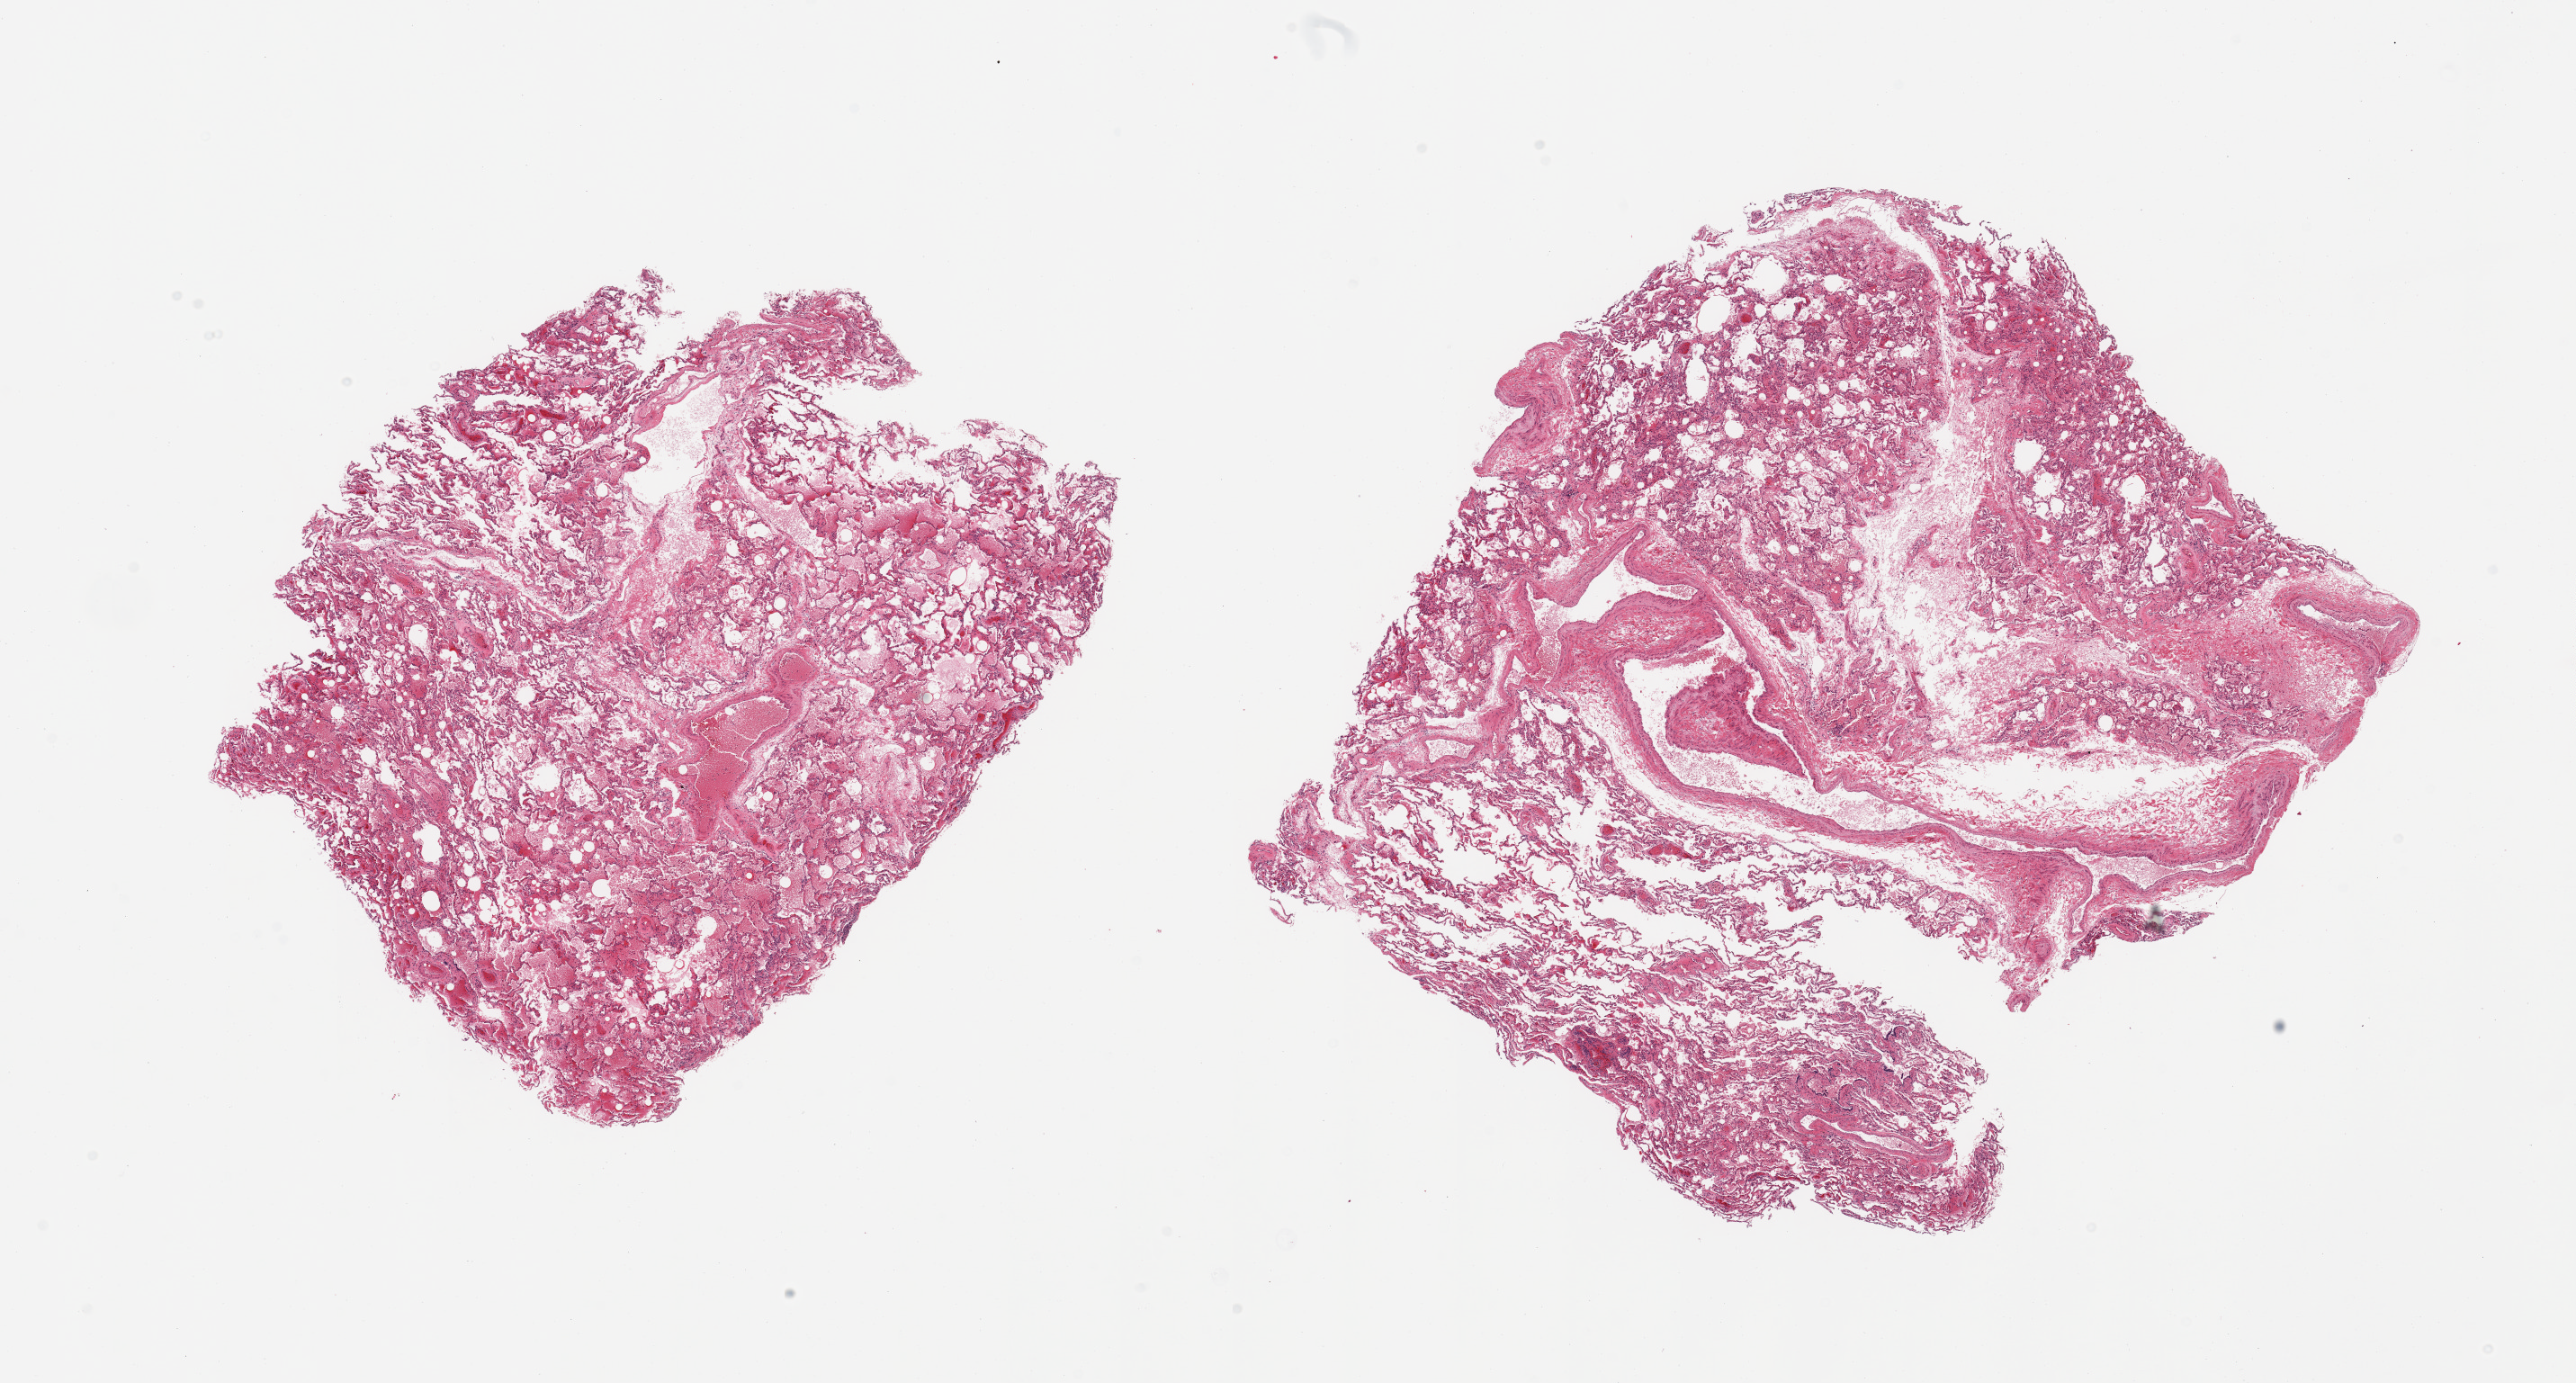
Haematoxylin and eosin whole-slide image — whole scanned area (about 22.6 x 12.2 mm, slide scanned at 20x) shown as a low-resolution overview; PAXgene-fixed, paraffin-embedded tissue; target tissue: lung; donor tissue sample. Donor sex: female.
• reviewer comment on this tissue sample: 2 pieces; prominent pulmonary edema and alveolar hemorrhage